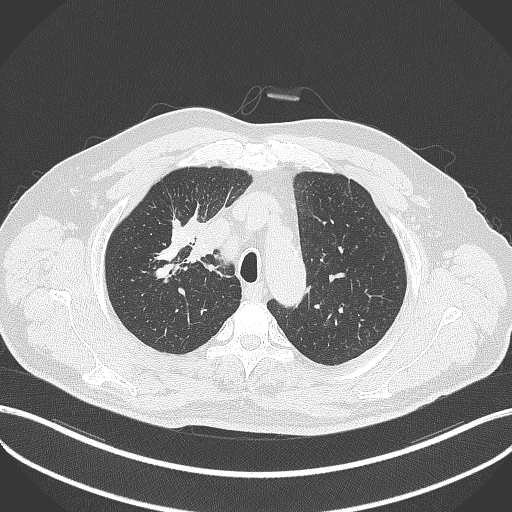
Chest CT, one axial slice; slice 308 of 411 in the series (ordered by position); reconstruction kernel B70f; lung window (W 1500 / L -600 HU); 1 mm slice thickness; 512 × 512 image matrix, field of view 400 × 400 mm. Patient: male, 60 years. From the clinical record (not read from this slice): clinical TNM (as recorded): T1b N1 M0.
Structures marked on this image (bounding box drawn by a radiologist):
- lung tumour (recorded histology: squamous cell carcinoma): box from (x=186, y=232) to (x=209, y=267) px